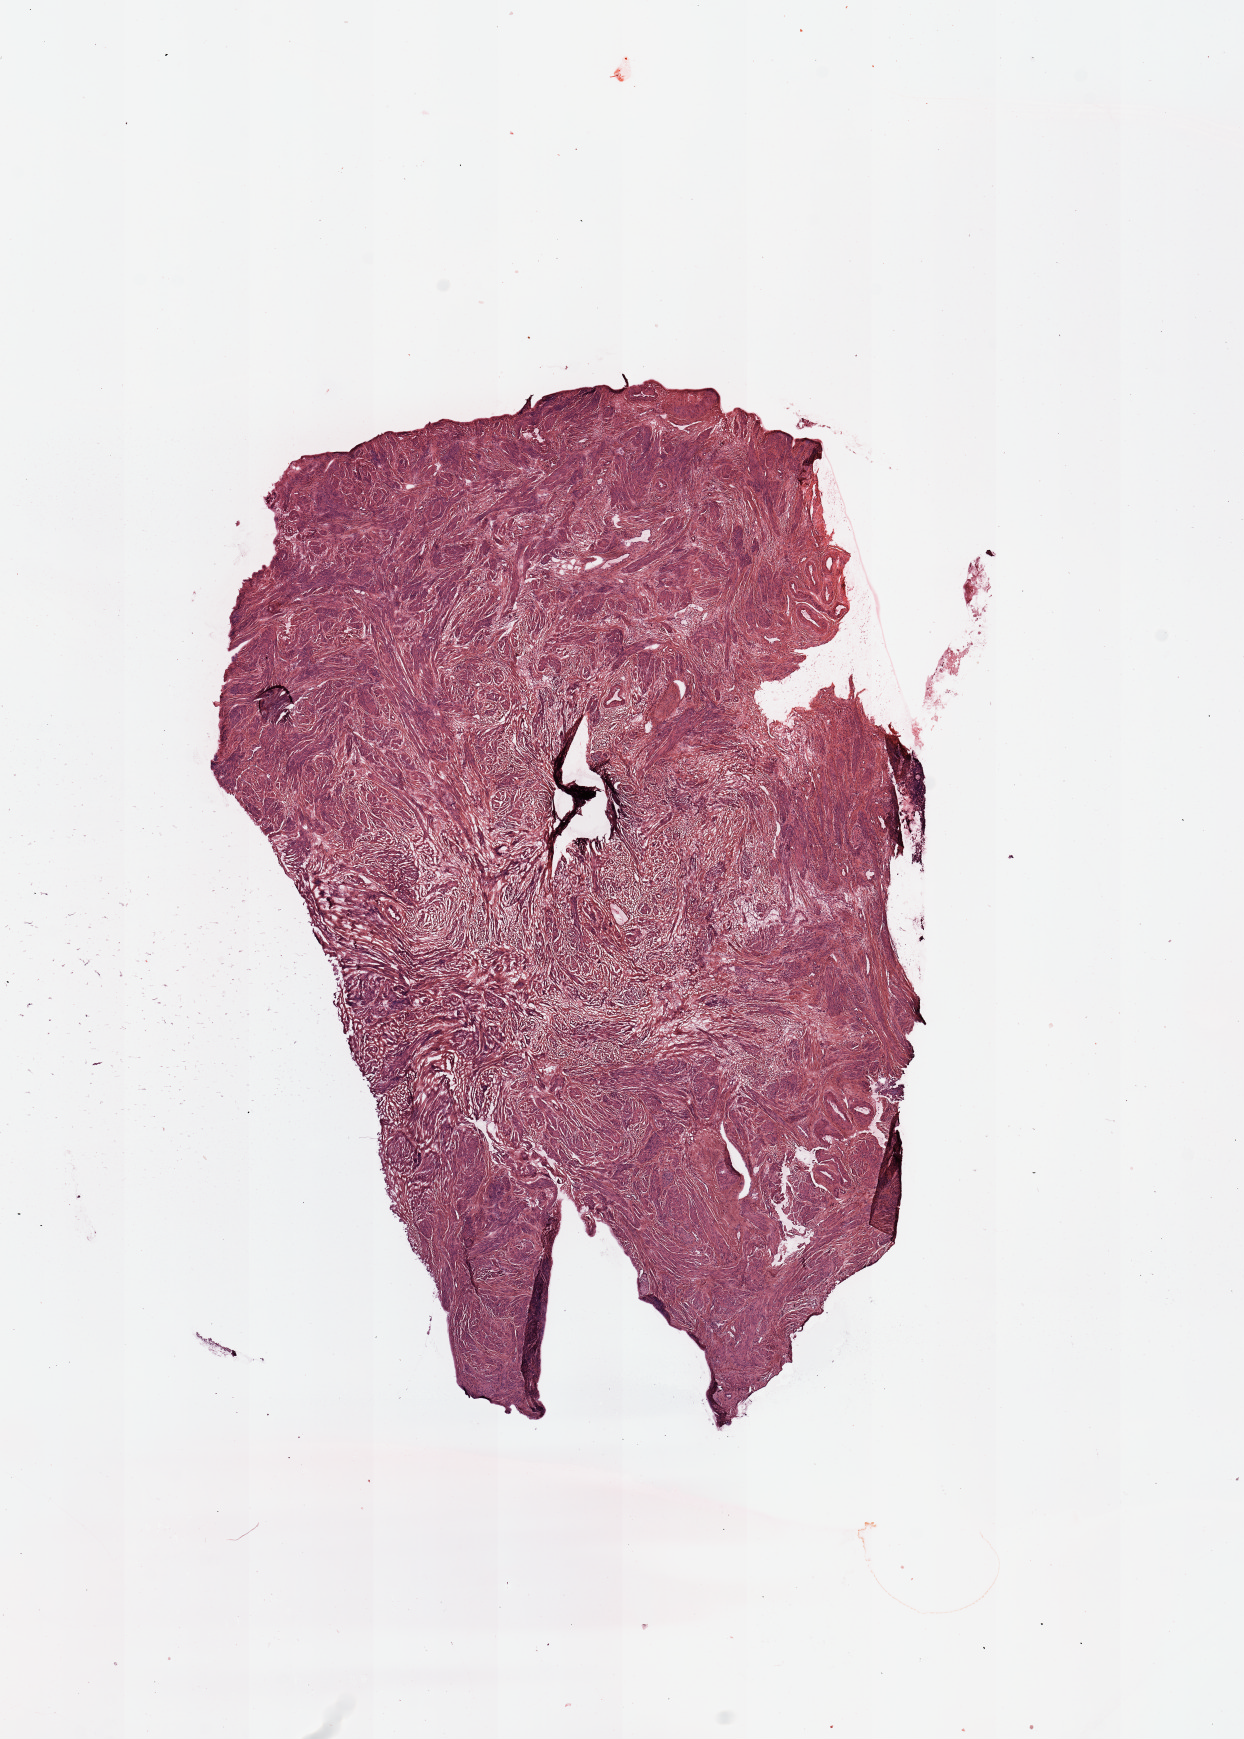
Digitized H&E tissue section (whole slide), whole scanned area (about 9.8 x 13.8 mm, acquisition: 20x scan) shown as a low-resolution overview, normal (non-tumour) tissue sample, uterus. Patient: female, age 65 years.
This section: normal (non-tumour) tissue from the same patient. Patient diagnosis: Endometrioid adenocarcinoma, NOS.